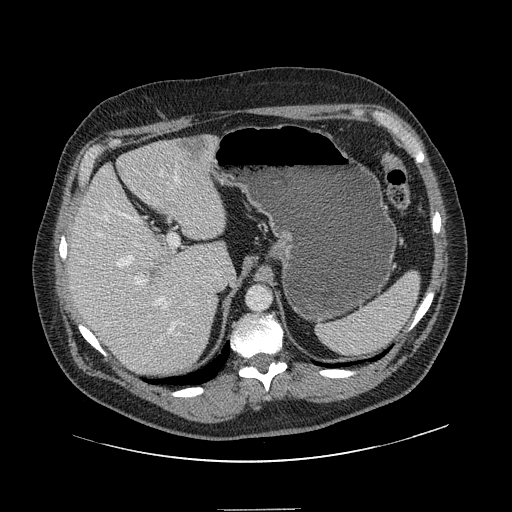
Contrast-enhanced abdominal CT, one axial slice. Slice 102 of 154 in the series (ordered by position). Soft-tissue window (W 400 / L 40 HU). 2.5 mm slice thickness. 512 × 512 image matrix, field of view 451 × 451 mm. Male patient, age 61 years. Case-level facts recorded for this patient, not image findings: diagnosis: colorectal cancer liver metastases, imaged before liver resection; multiple liver metastases: yes.
Outlined on this slice (manually delineated by an expert):
- hepatic veins: bounding box <96,175,184,338> (left, top, right, bottom; pixels)
- liver: <68,136,226,378>
- planned liver remnant (the part of the liver to remain after resection): <68,144,226,360>
- portal vein (with intrahepatic branches): <105,170,176,285>
- liver metastasis: <179,139,205,163>